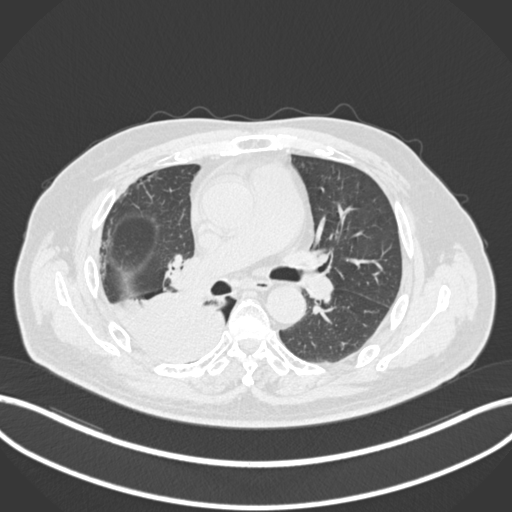
Chest CT, one axial slice. Slice 109 of 218 in the series (ordered by position). 120 kVp. Lung window (W 1500 / L -600 HU). 1 mm slice thickness. 512 × 512 image matrix, field of view 400 × 400 mm. Patient: male, 68 years. From the clinical record (not read from this slice): clinical TNM (as recorded): T2a N0 M0.
Annotated regions visible in this slice (bounding box drawn by a radiologist):
- lung tumour (recorded histology: adenocarcinoma): box from (x=110, y=288) to (x=226, y=374) px